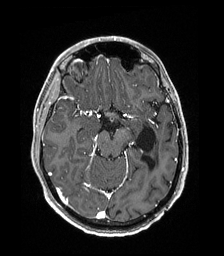
Brain MRI from a brain-tumour surgery series, one axial slice; slice 112 of 192 in the series (ordered by position); T1-weighted post-contrast; 1 mm slice thickness; 224 × 256 image matrix. From the clinical record (not read from this slice): histopathology: Low grade glioma; IDH mutation: no; tumour location: Left Parieto-Occipital Intraventricular.
Structures marked on this image (manually delineated by an expert):
- previous resection cavity: bounding box (x1, y1, x2, y2) in pixels: (135, 127, 156, 171)